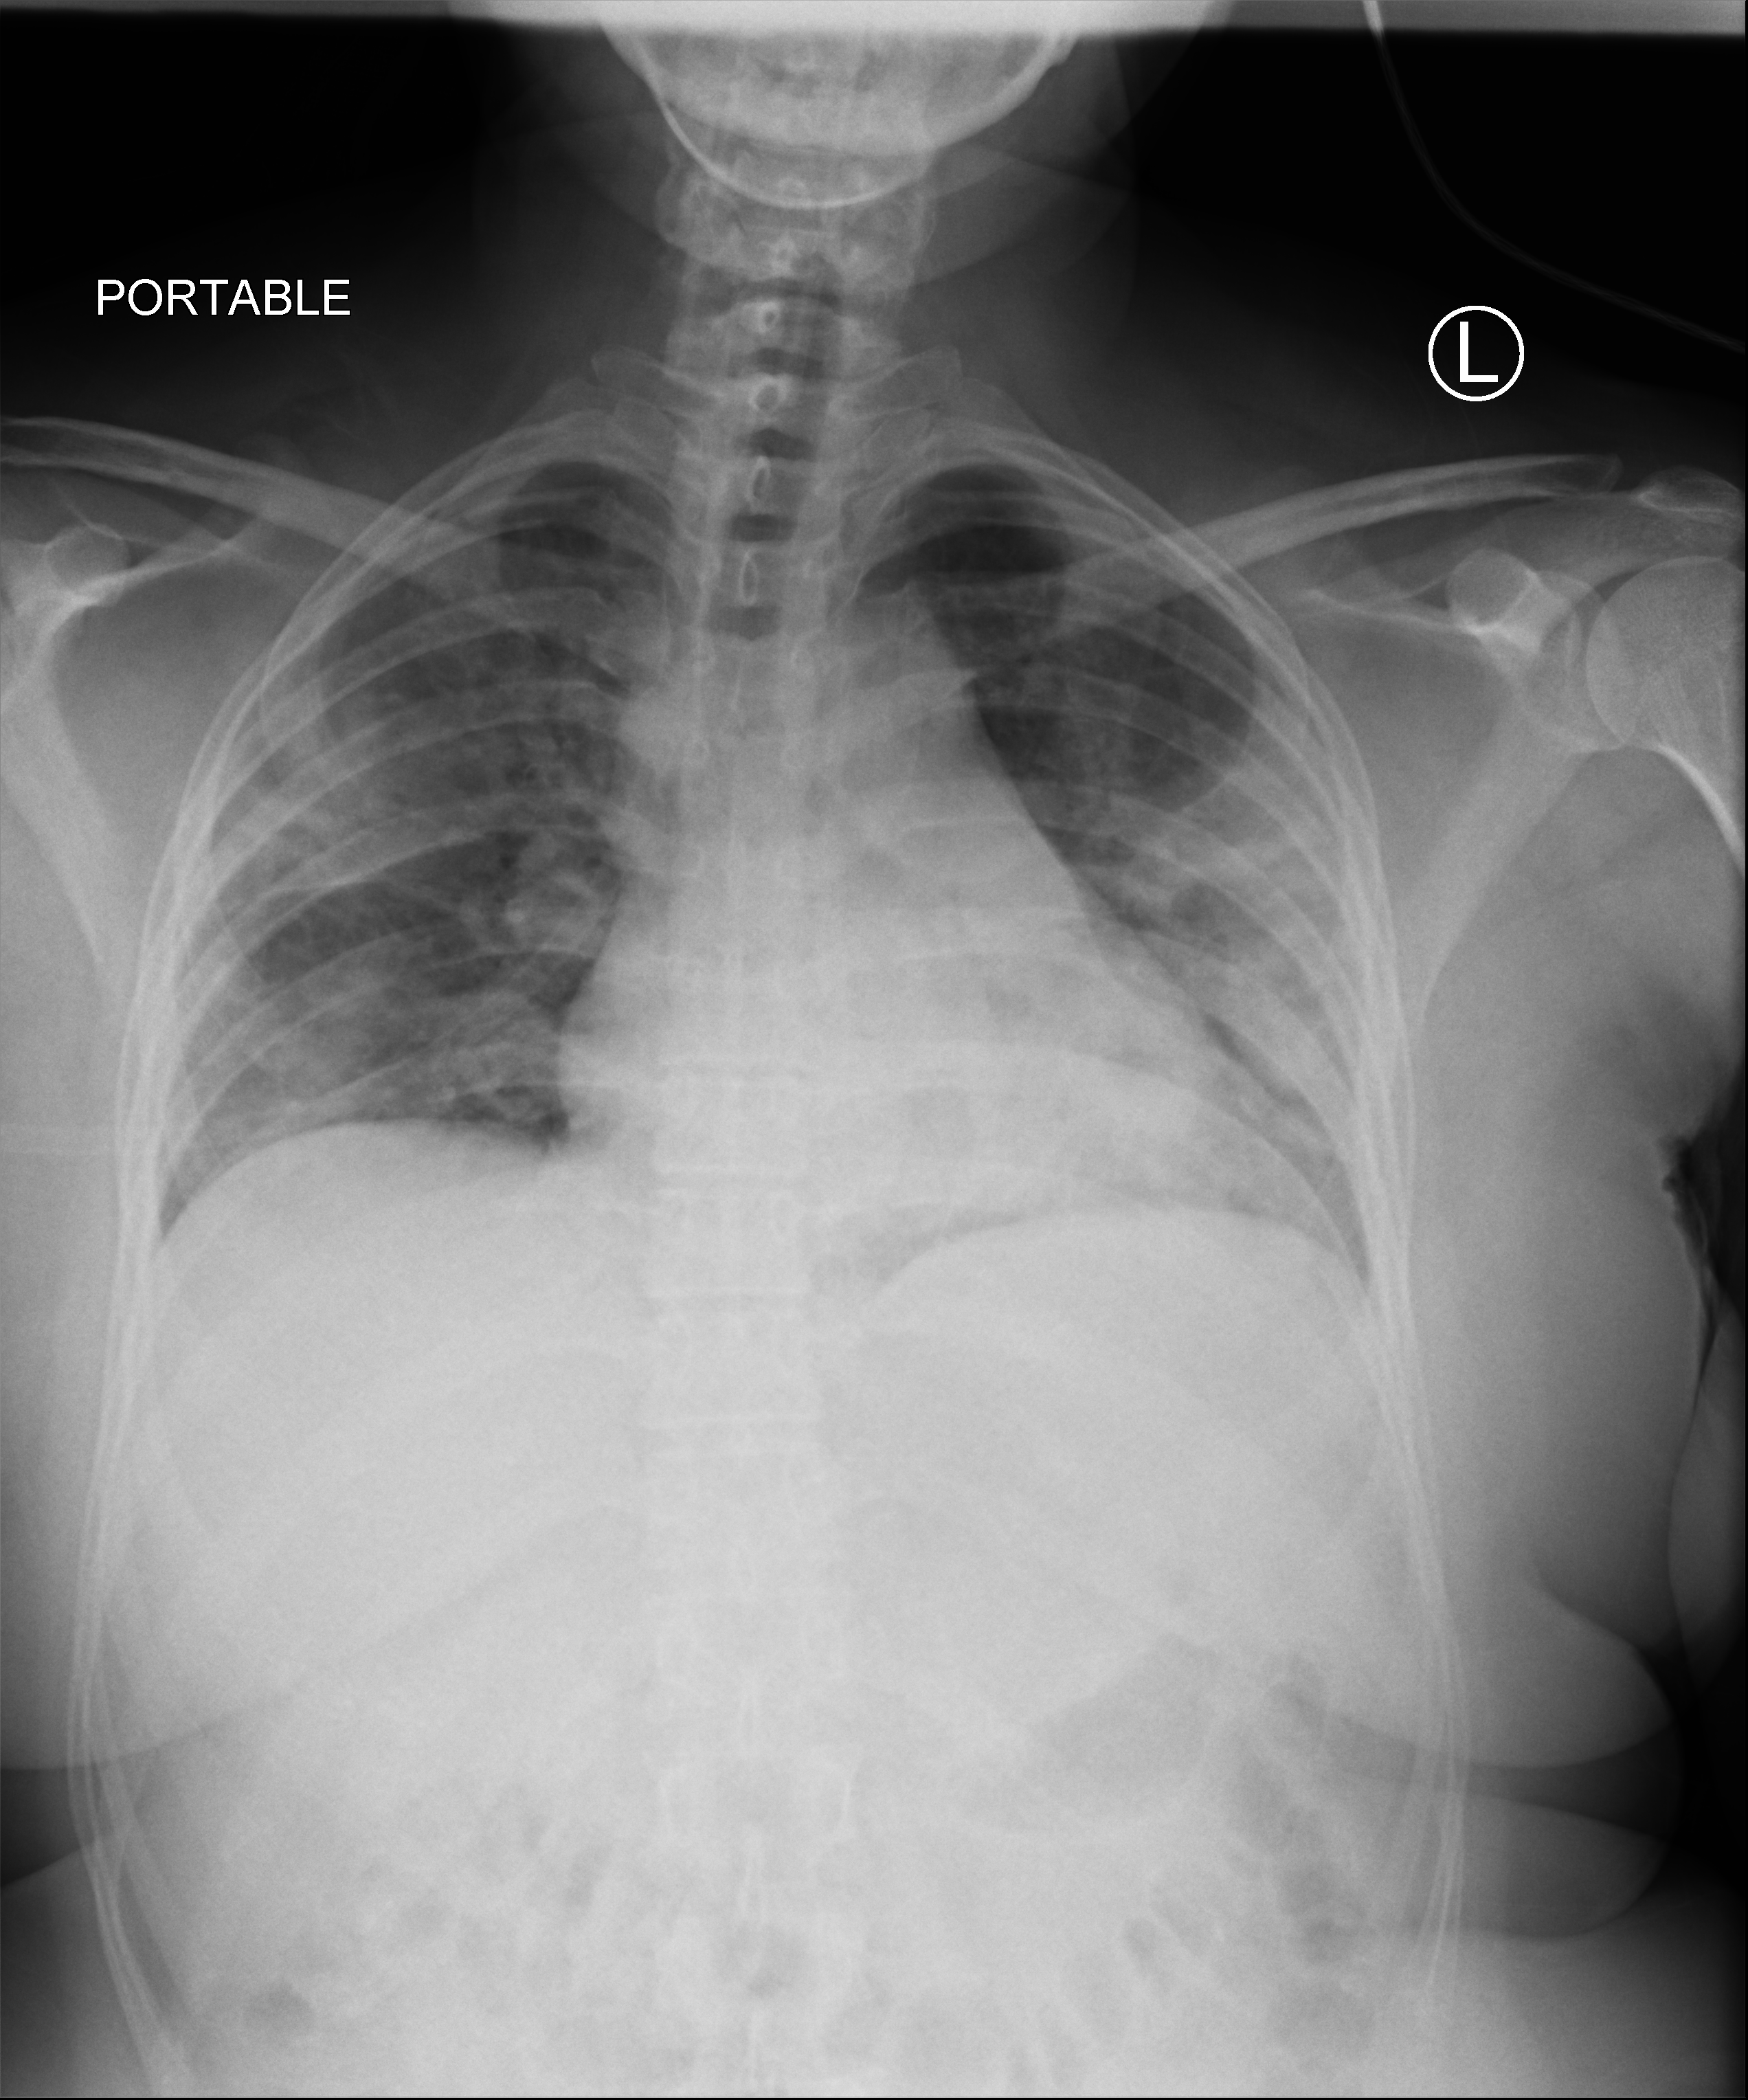
Bedside chest radiograph (computed radiography); anteroposterior (AP) projection. Patient hospitalised with COVID-19; female, aged 18–59 years.
Hospital-stay facts (about this admission, not read from this image; timing relative to this image not recorded): chronic kidney disease (admission record): no.